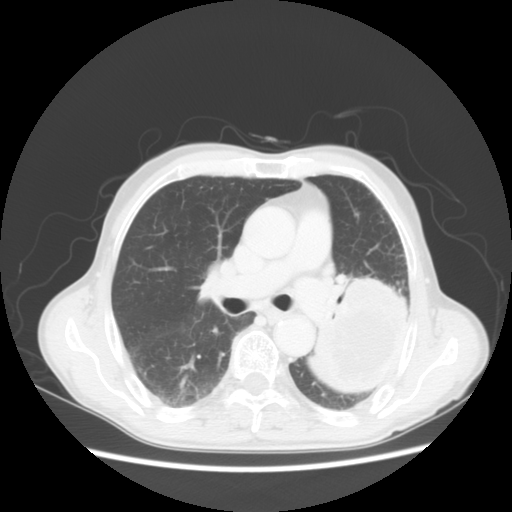
Chest CT, one axial slice. Position 31 of 51 along the scan axis. 120 kVp. Lung window (W 1500 / L -600 HU). 512 × 512 image matrix, field of view 360 × 360 mm. Patient: male, 64 years. From the clinical record (not read from this slice): clinical TNM (as recorded): T4 N0 M0; histopathological grade: G2-3.
Outlined on this slice (rectangle marked by the reading radiologist):
- lung tumour (recorded histology: squamous cell carcinoma): bounding box [x1, y1, x2, y2] px = [318, 270, 413, 415]